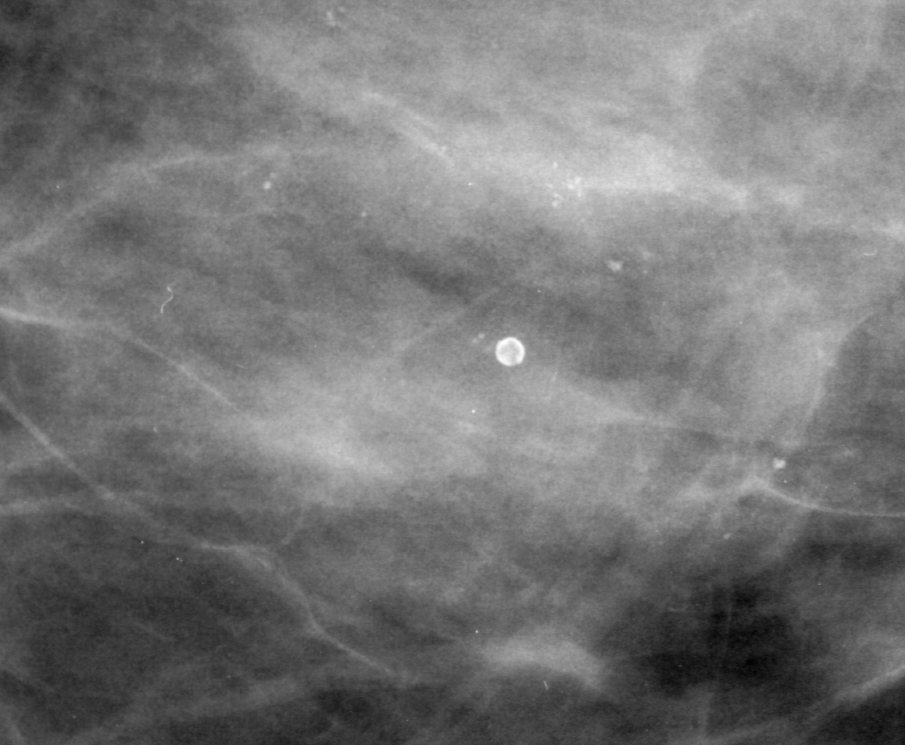
Crop from a digitized film mammogram around one marked abnormality; right breast; CC view; BI-RADS breast density category 4 (scale 1–4).
Marked abnormality: calcifications, morphology pleomorphic, distribution linear; BI-RADS assessment category 4; subtlety rating 3 on a 1 (subtle) to 5 (obvious) scale; pathology (as recorded): benign.